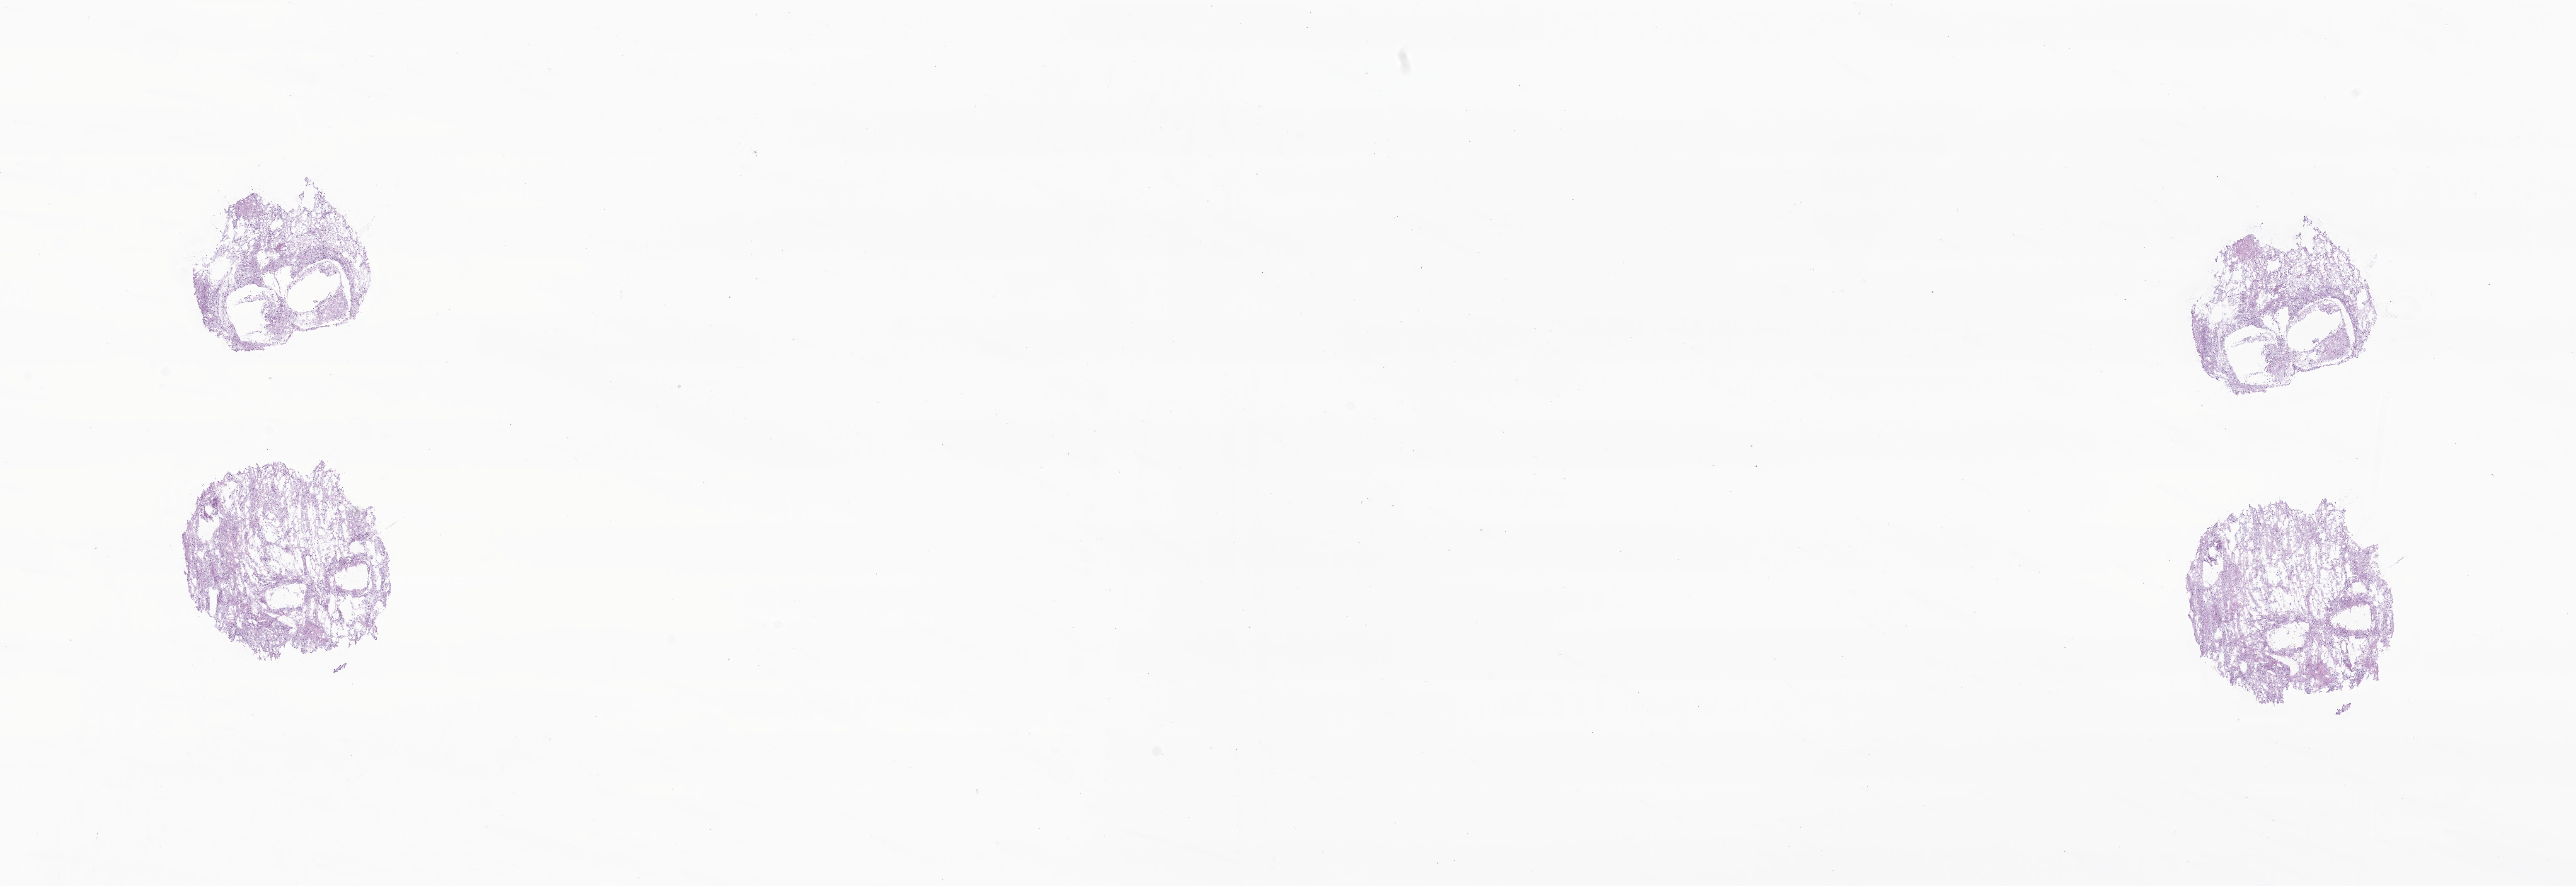
Digitized hematoxylin and eosin (H&E)-stained section of tumor tissue from the brain, shown as a low-resolution overview of the whole scanned area (about 26.2 x 9.0 mm), frozen section (OCT-embedded). Patient: male, age 90 months.
Recorded diagnosis: Neoplasm, uncertain whether benign or malignant.